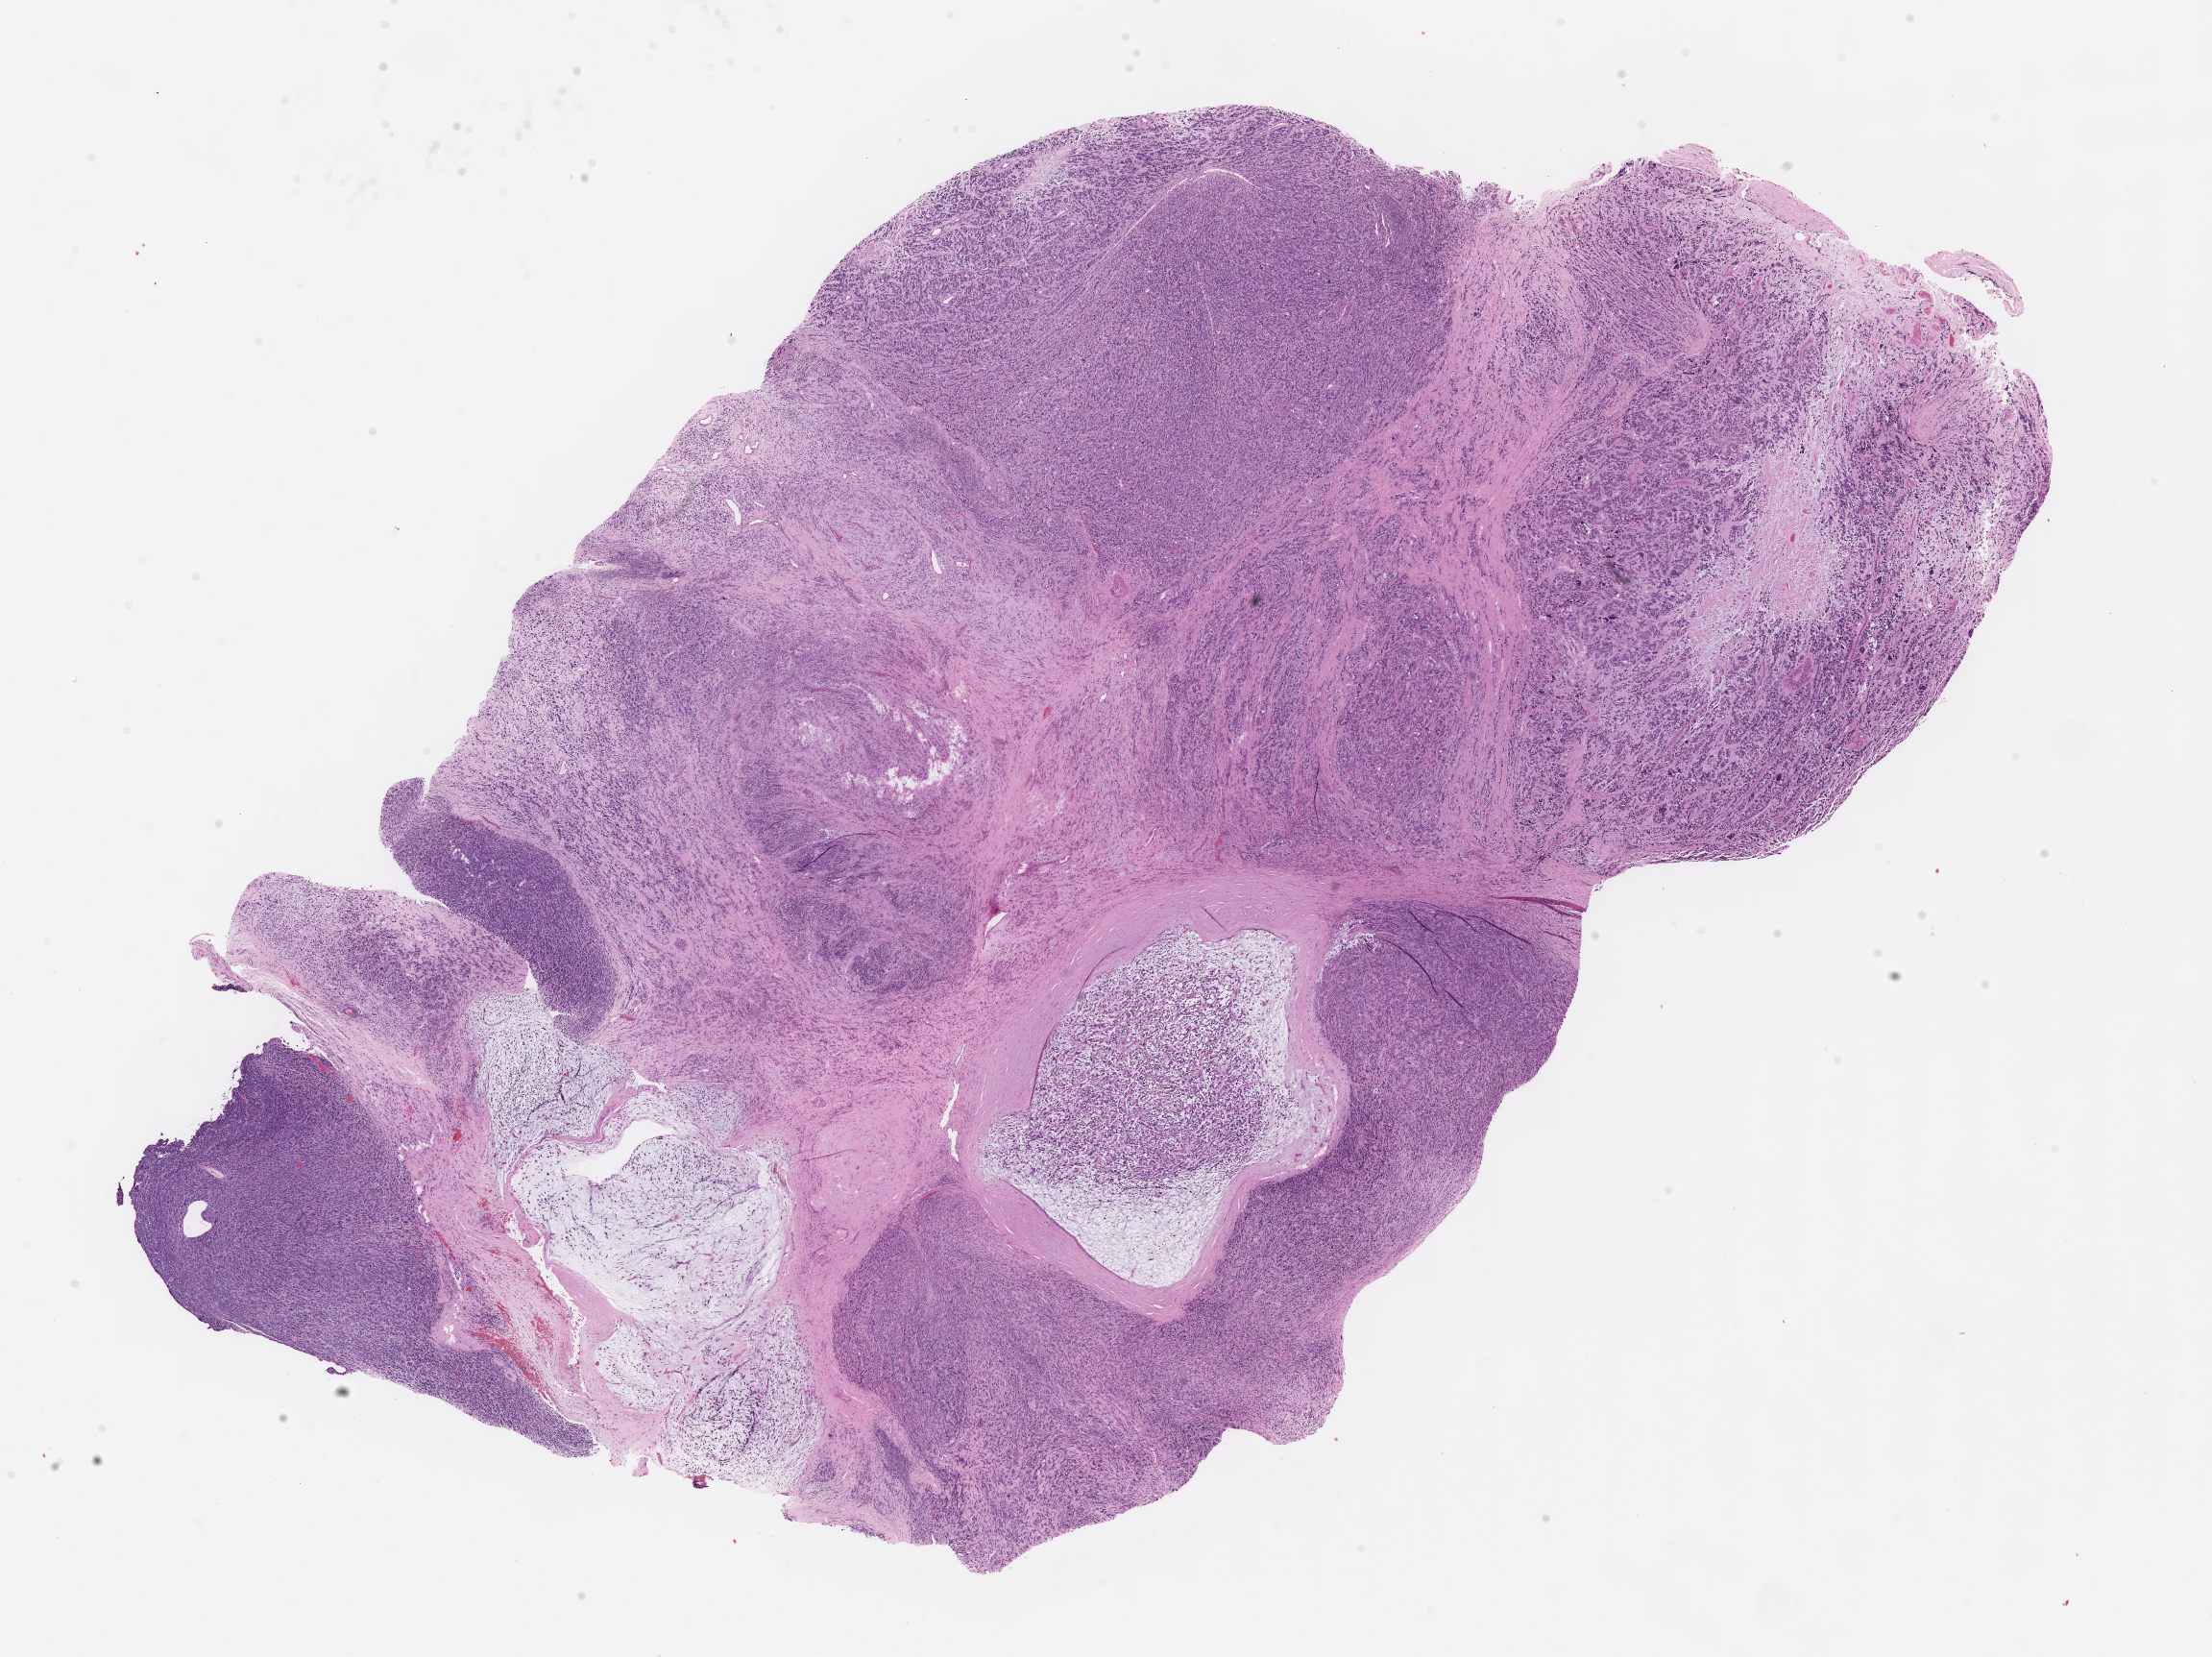
Digitized haematoxylin and eosin-stained section of tumor tissue, a low-resolution overview of the entire scanned area, about 18.6 x 13.9 mm. Formalin-fixed paraffin-embedded section. Sample anatomic site: groin mass, left. Female patient, age at diagnosis 2.6 years.
• primary site (case record): thigh
• stage (as recorded): 3
• diagnosis: rhabdomyosarcoma; histological classification: embryonal rhabdomyosarcoma